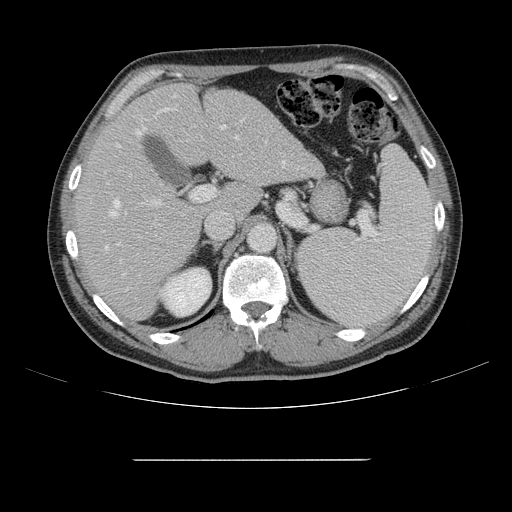
Contrast-enhanced abdominal CT, one axial slice. Position 97 of 164 along the scan axis. 120 kVp. Intravenous contrast given. Soft-tissue window (W 400 / L 40 HU). 2.5 mm slice thickness. 512 × 512 image matrix, field of view 404 × 404 mm. Male patient, age 54 years. From the clinical record (not read from this slice): diagnosis: colorectal cancer liver metastases, imaged before liver resection; multiple liver metastases: yes; largest metastasis: 1 cm; disease in both lobes: no.
Outlined on this slice (outlined manually by an expert reader):
- hepatic veins: bounding box <105,131,285,276> (left, top, right, bottom; pixels)
- liver: <77,85,321,320>
- planned liver remnant (the part of the liver to remain after resection): <77,85,235,320>
- portal vein (with intrahepatic branches): <117,95,227,204>